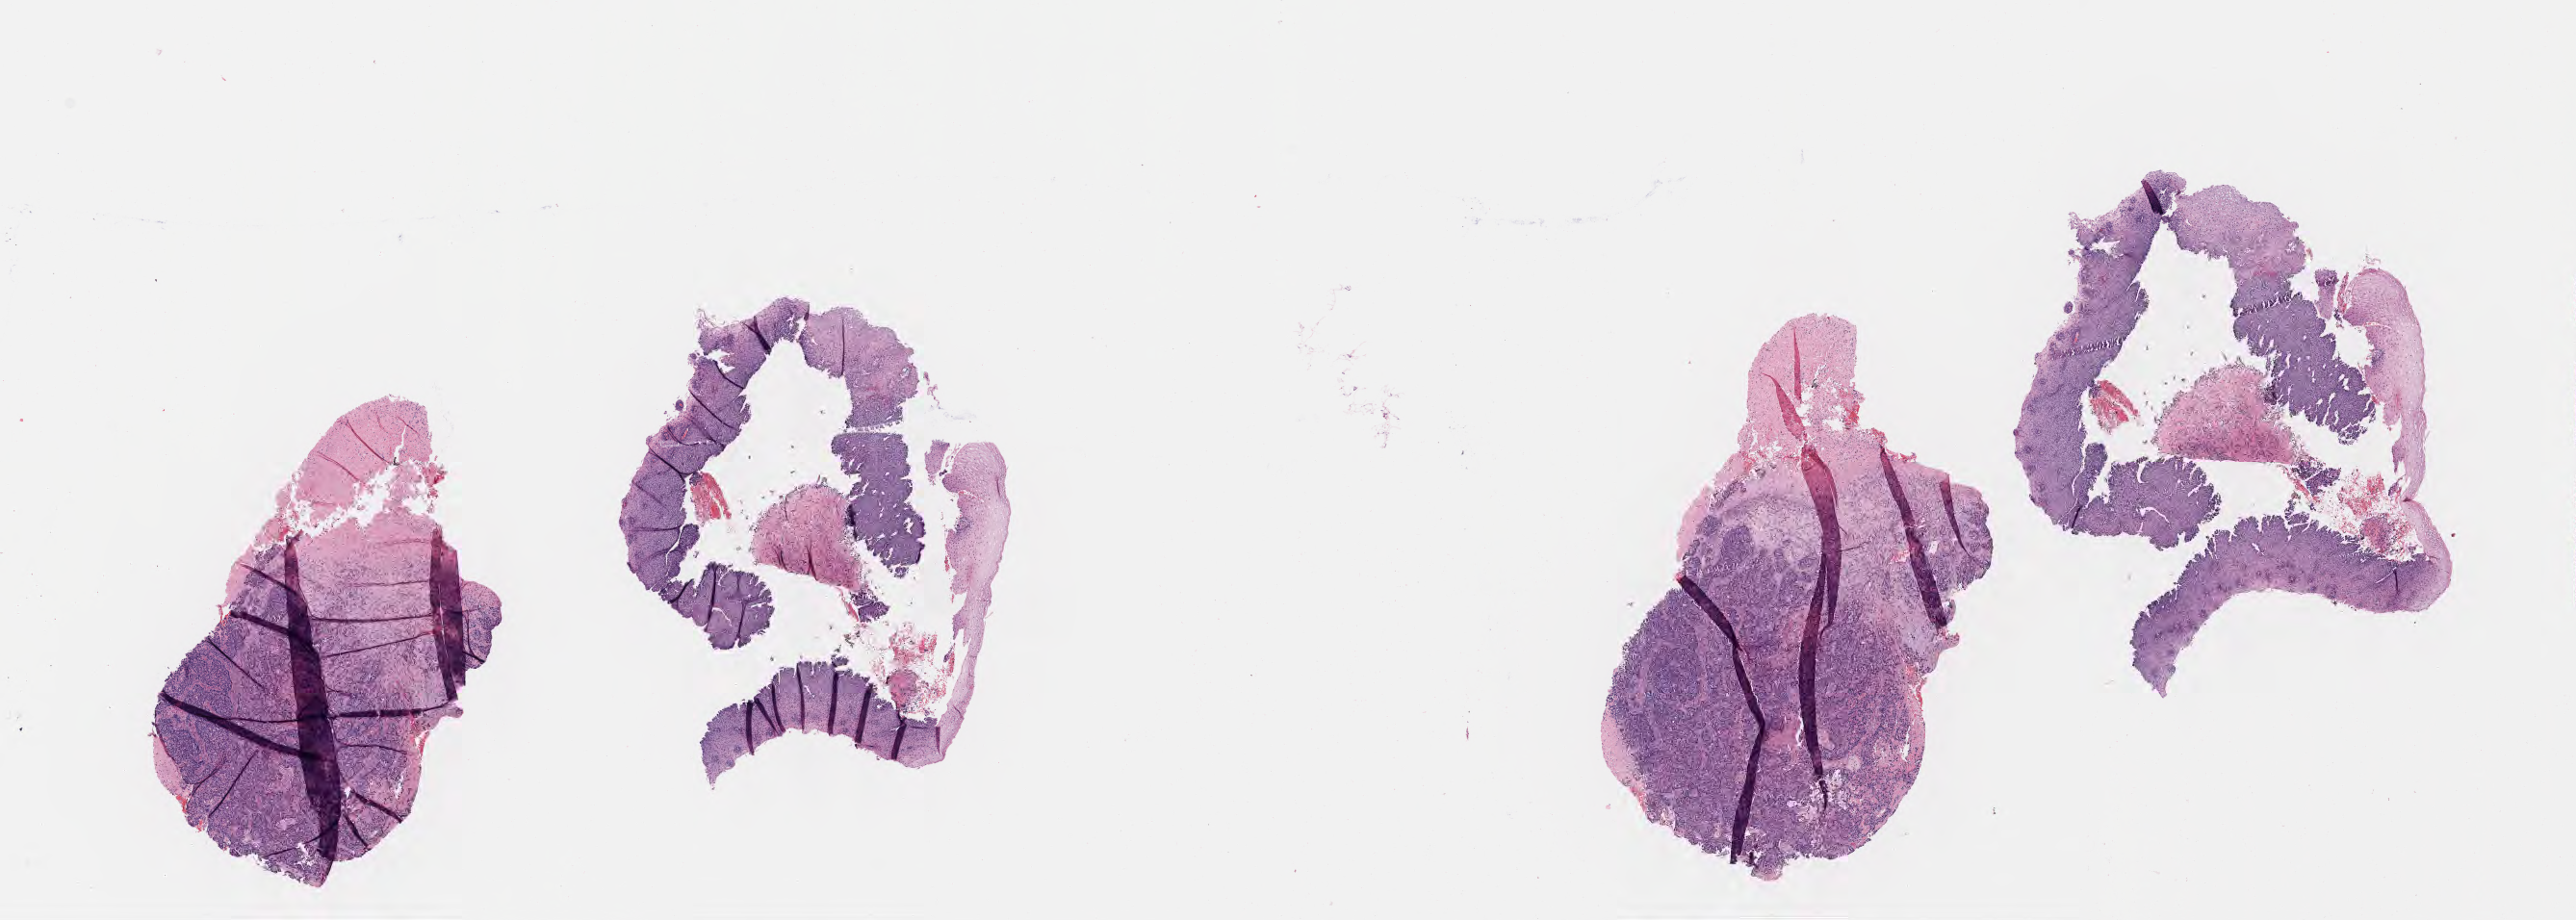
Whole-slide image, haematoxylin and eosin stain, whole scanned area (about 21.6 x 7.7 mm) shown as a low-resolution overview; tumor tissue; anatomic site: cervix. Female patient, aged 57.
- diagnosis: Squamous cell carcinoma, large cell, nonkeratinizing, NOS